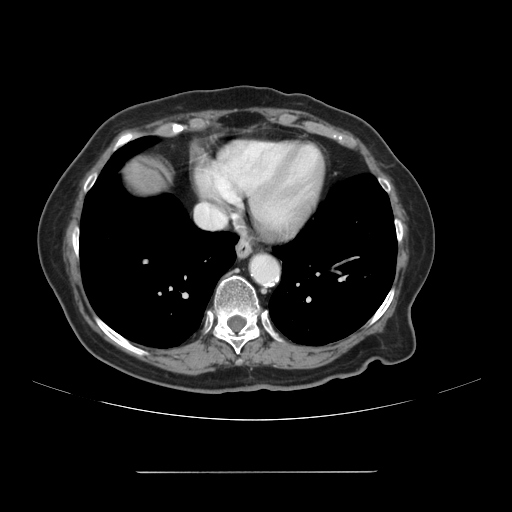
Contrast-enhanced abdominal CT, one axial slice. Slice 109 of 111 in the series (ordered by position). Intravenous contrast given. Soft-tissue window (W 400 / L 40 HU). 2.5 mm slice thickness. 512 × 512 image matrix, field of view 400 × 400 mm. Female patient, age 74 years. From the clinical record (not read from this slice): diagnosis: colorectal cancer liver metastases, imaged before liver resection; multiple liver metastases: yes; largest metastasis: 1.1 cm; disease in both lobes: yes.
Structures marked on this image (outlined manually by an expert reader):
- liver: bounding box [x1, y1, x2, y2] px = [120, 157, 170, 197]